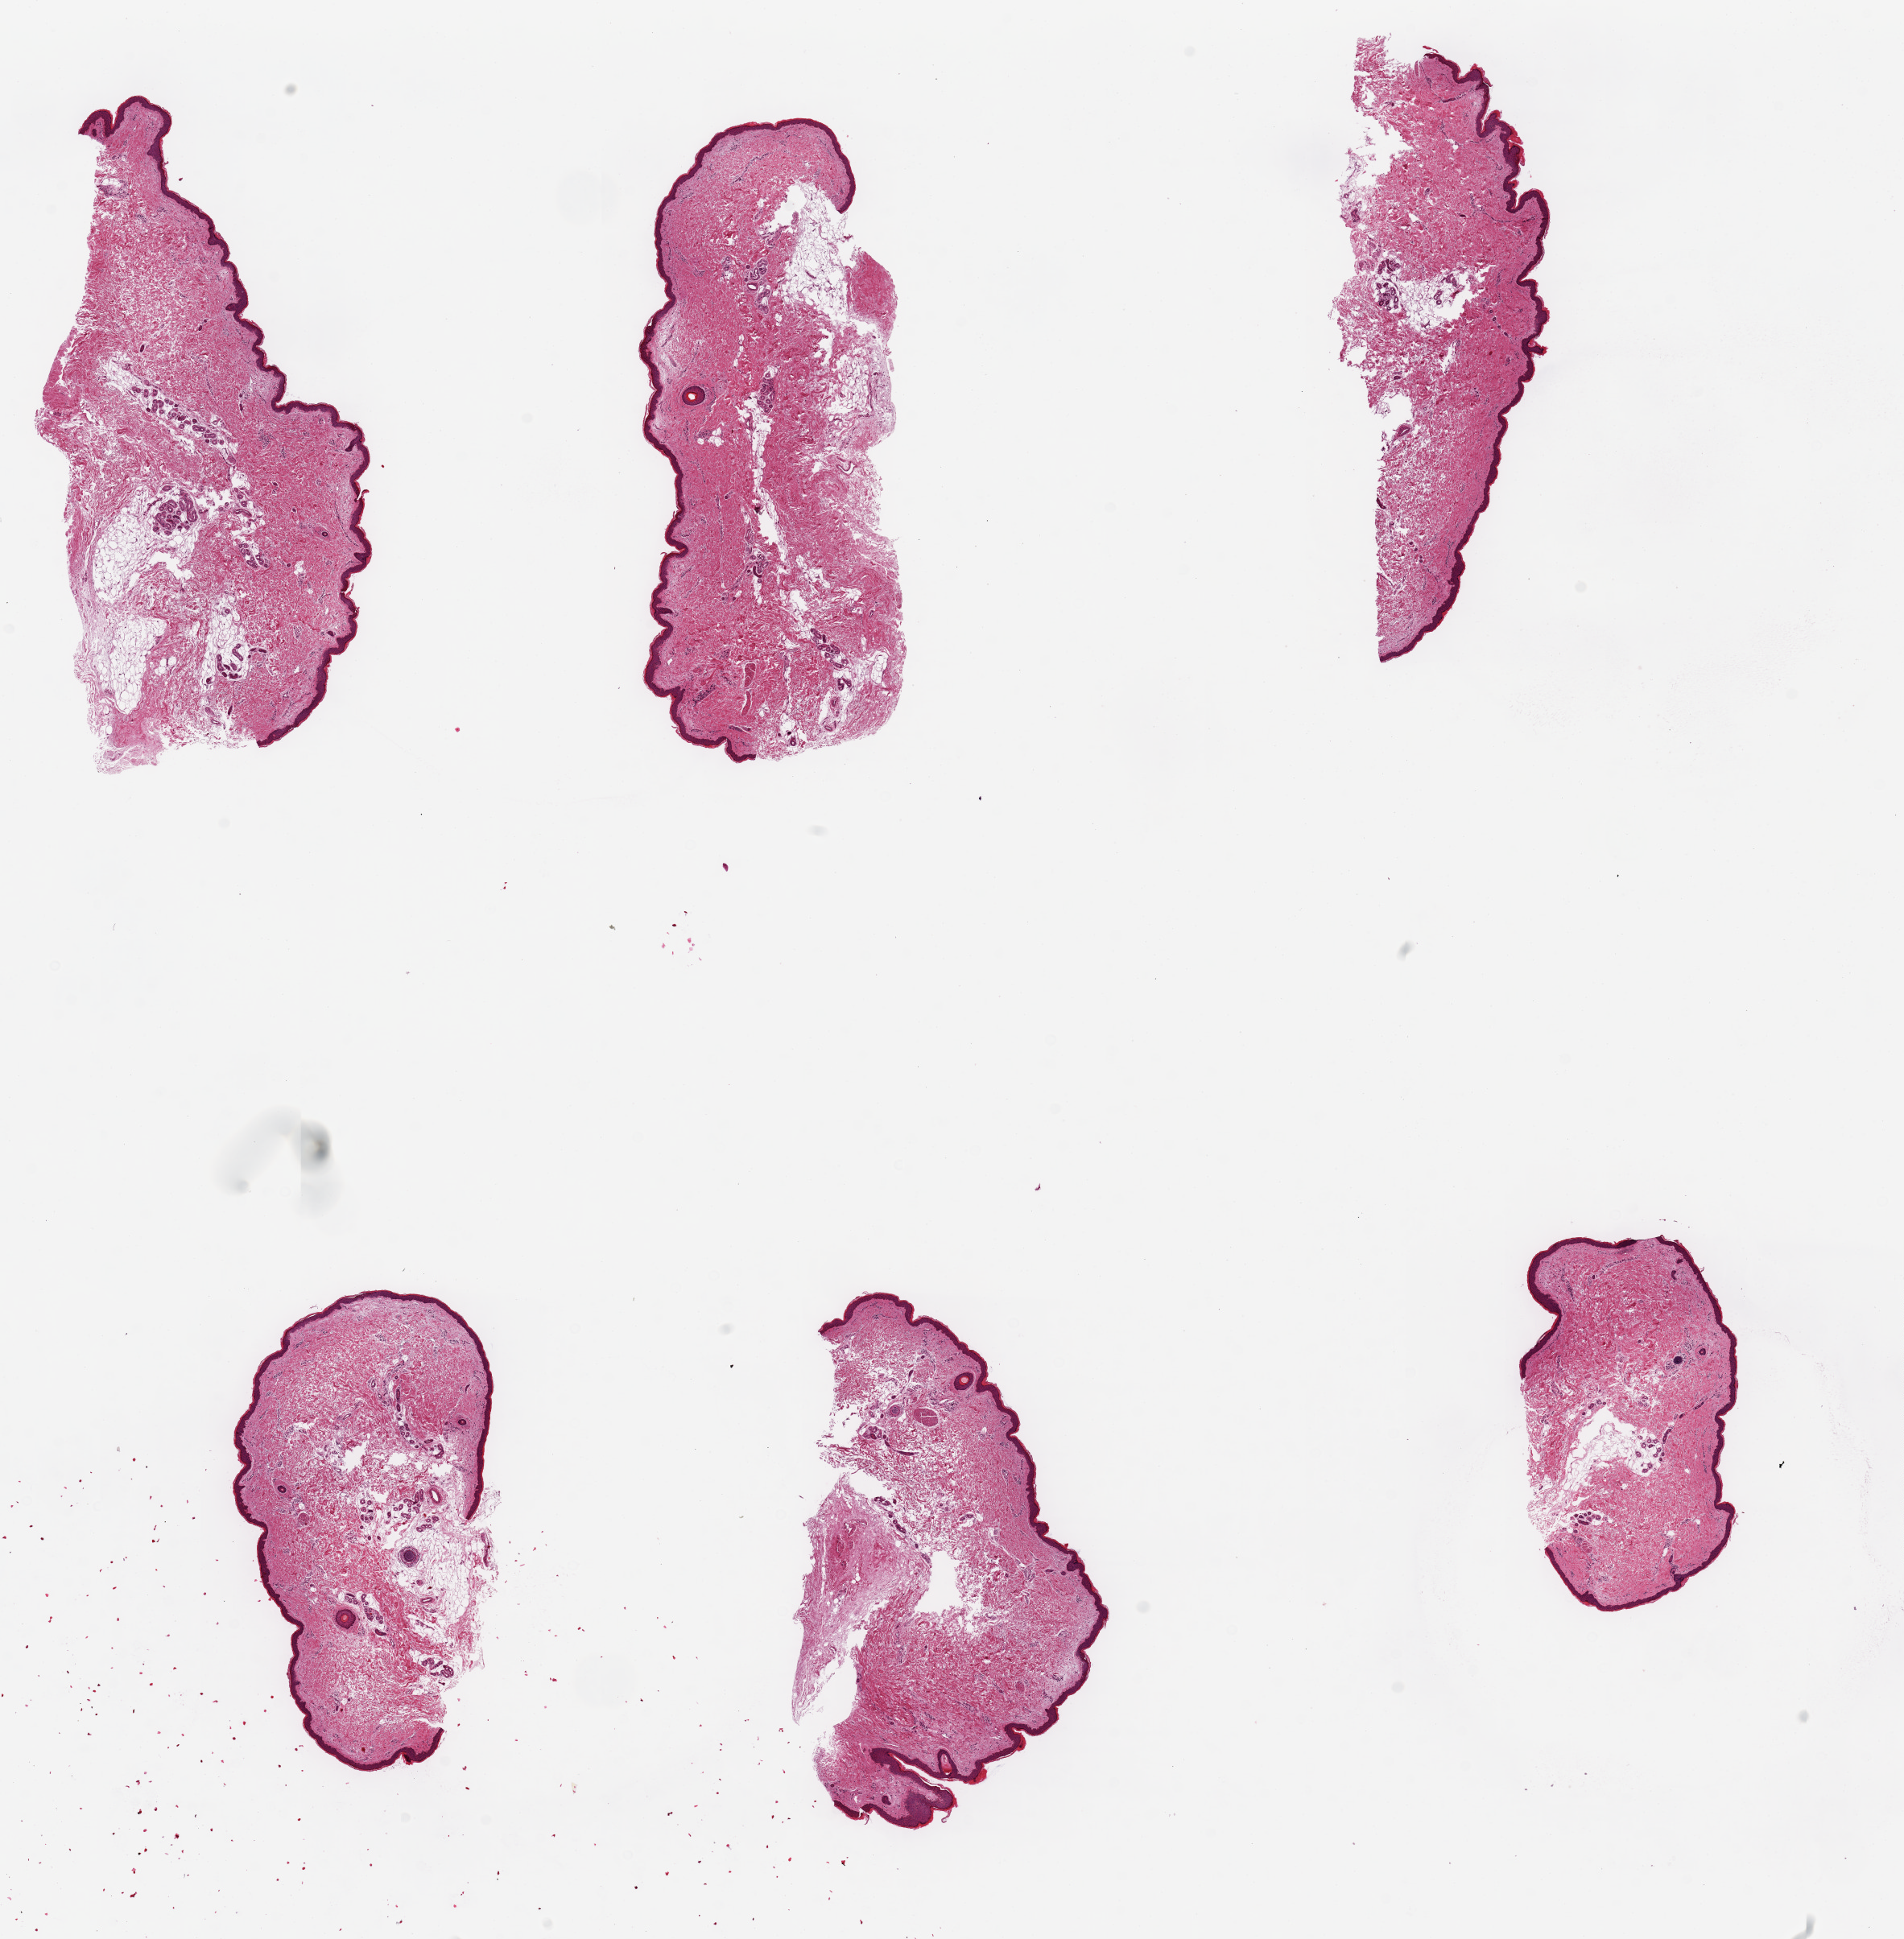
Whole-slide image, H&E stain — shown as a low-resolution overview of the whole scanned area (about 18.7 x 19.1 mm, slide scanned at 20x); PAXgene-fixed, paraffin-embedded tissue; target tissue: skin of lower leg; tissue donor sample. Donor: male.
Review note (as recorded): 6 pieces, up to 6.5x3mm; Well trimmed of subcutaneous adipose.